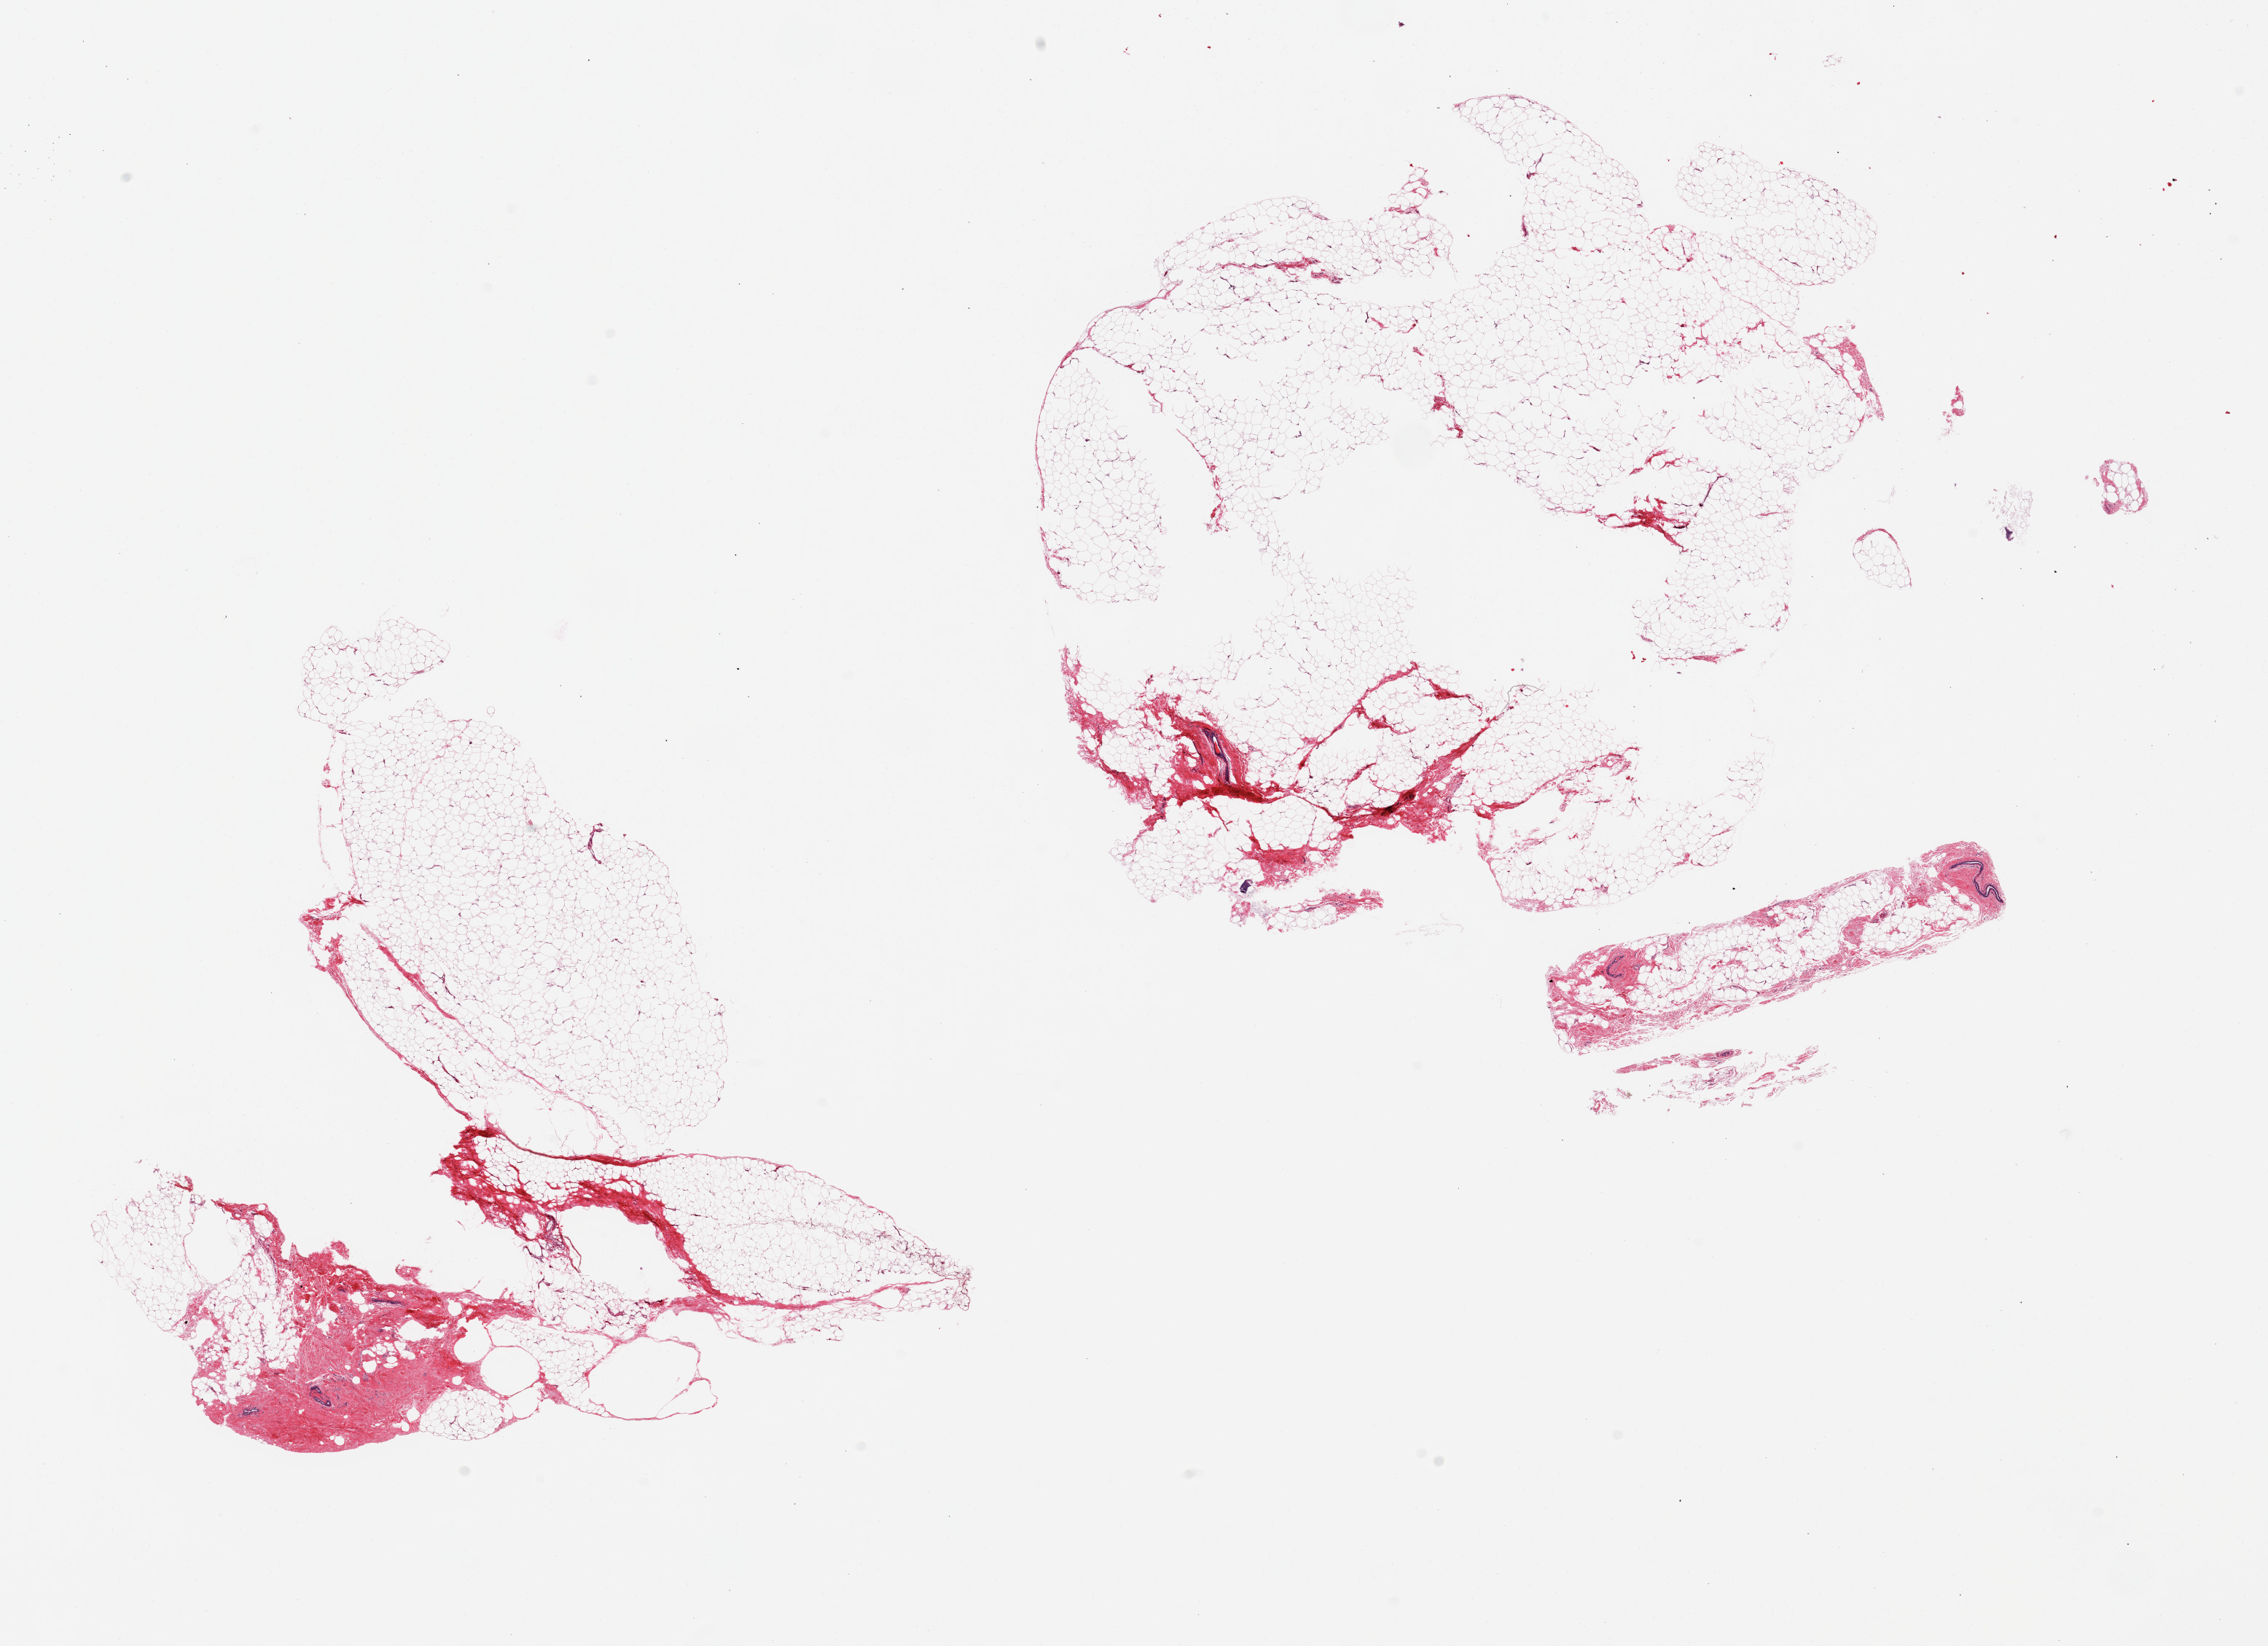
Whole-slide image, haematoxylin and eosin stain — a low-resolution overview of the entire scanned area, about 24.6 x 17.9 mm (from a 20x scan). PAXgene-fixed paraffin-embedded (PFPE) section. Target tissue: breast. Donor tissue sample. Donor sex: female.
Reviewer comment on this tissue sample: 2 pieces, fibroadipose tissue; minute trace atrophic ductal elements present.